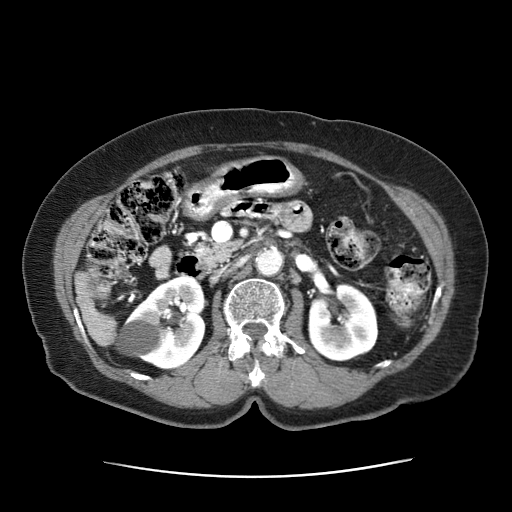
Contrast-enhanced abdominal CT (liver protocol), one axial slice; slice 11 of 63 in the series (ordered by position); reconstruction kernel STANDARD; 120 kVp; intravenous contrast given; soft-tissue window (W 400 / L 40 HU); 512 × 512 image matrix, field of view 360 × 360 mm. Female patient, age 79 years. Case-level facts recorded for this patient, not image findings: diagnosis: hepatocellular carcinoma (patient treated with transarterial chemoembolisation; whether this scan precedes or follows treatment is not stated here); TNM stage (as recorded): Stage-II; Child-Pugh class: B; tumour differentiation: well differentiated; tumour nodularity: multinodular.
Annotated regions visible in this slice (semi-automatic segmentation, software-assisted and operator-edited):
- abdominal aorta: bounding box <256,246,284,275> (left, top, right, bottom; pixels)
- liver parenchyma outside the tumour (the mass and vessels are separate outlines, so this box may not span the whole liver): <75,272,116,346>